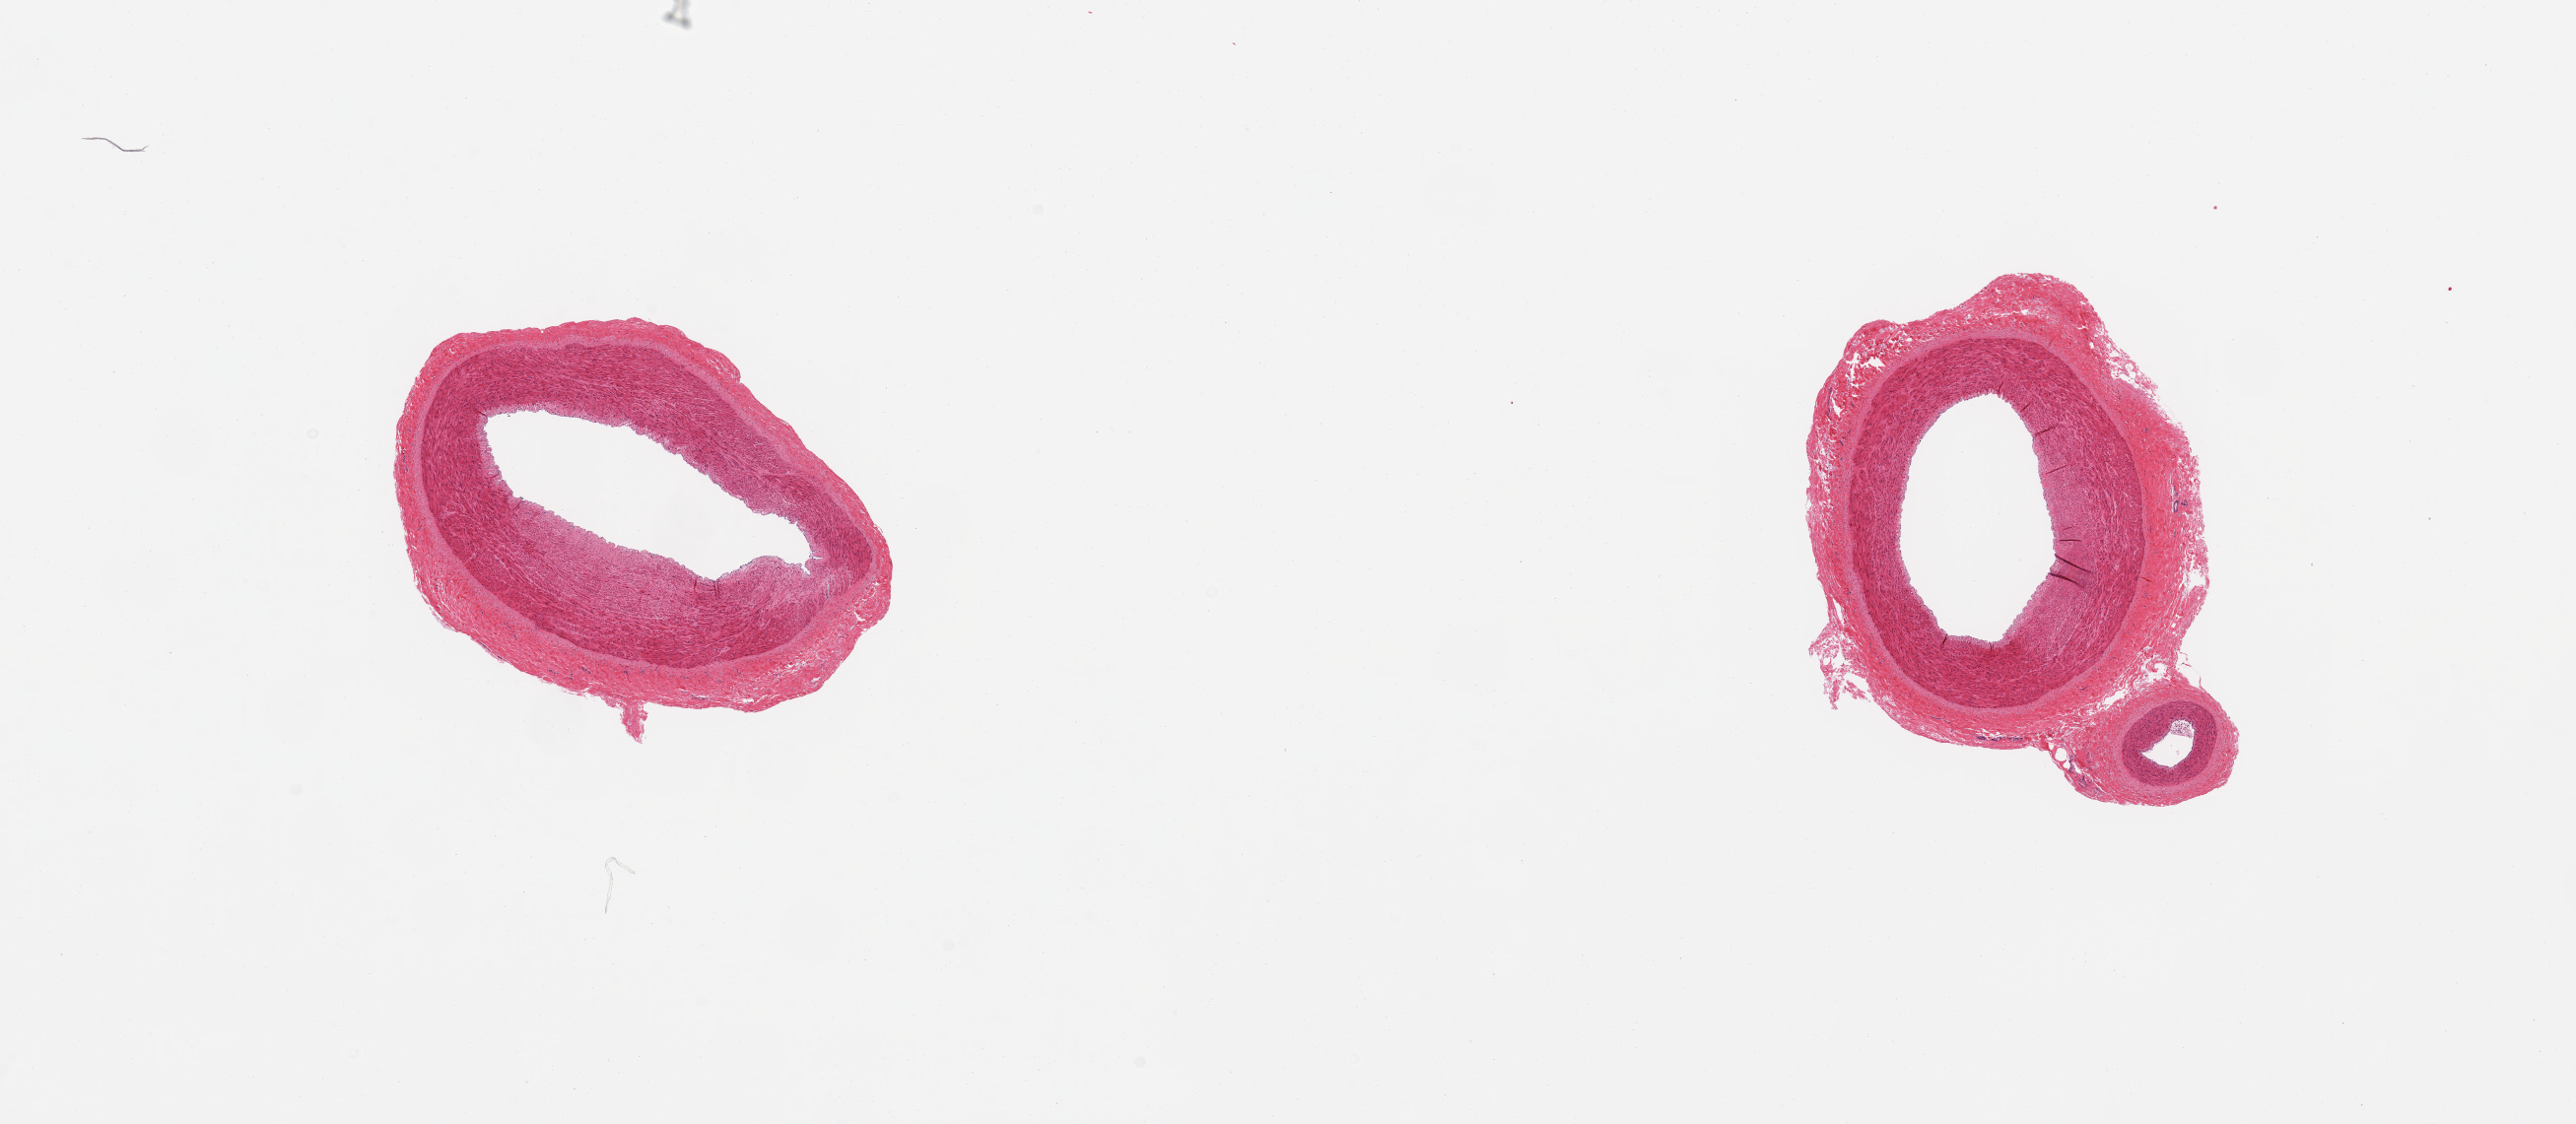
Haematoxylin and eosin whole-slide image, brightfield, whole scanned area (about 20.7 x 9.0 mm) shown as a low-resolution overview. PAXgene-fixed, paraffin-embedded tissue. Target tissue: tibial artery. Tissue donor sample. Donor: female.
* pathologist's review note for this sample: 2 pieces; well trimmed of fat, includes smaller branch